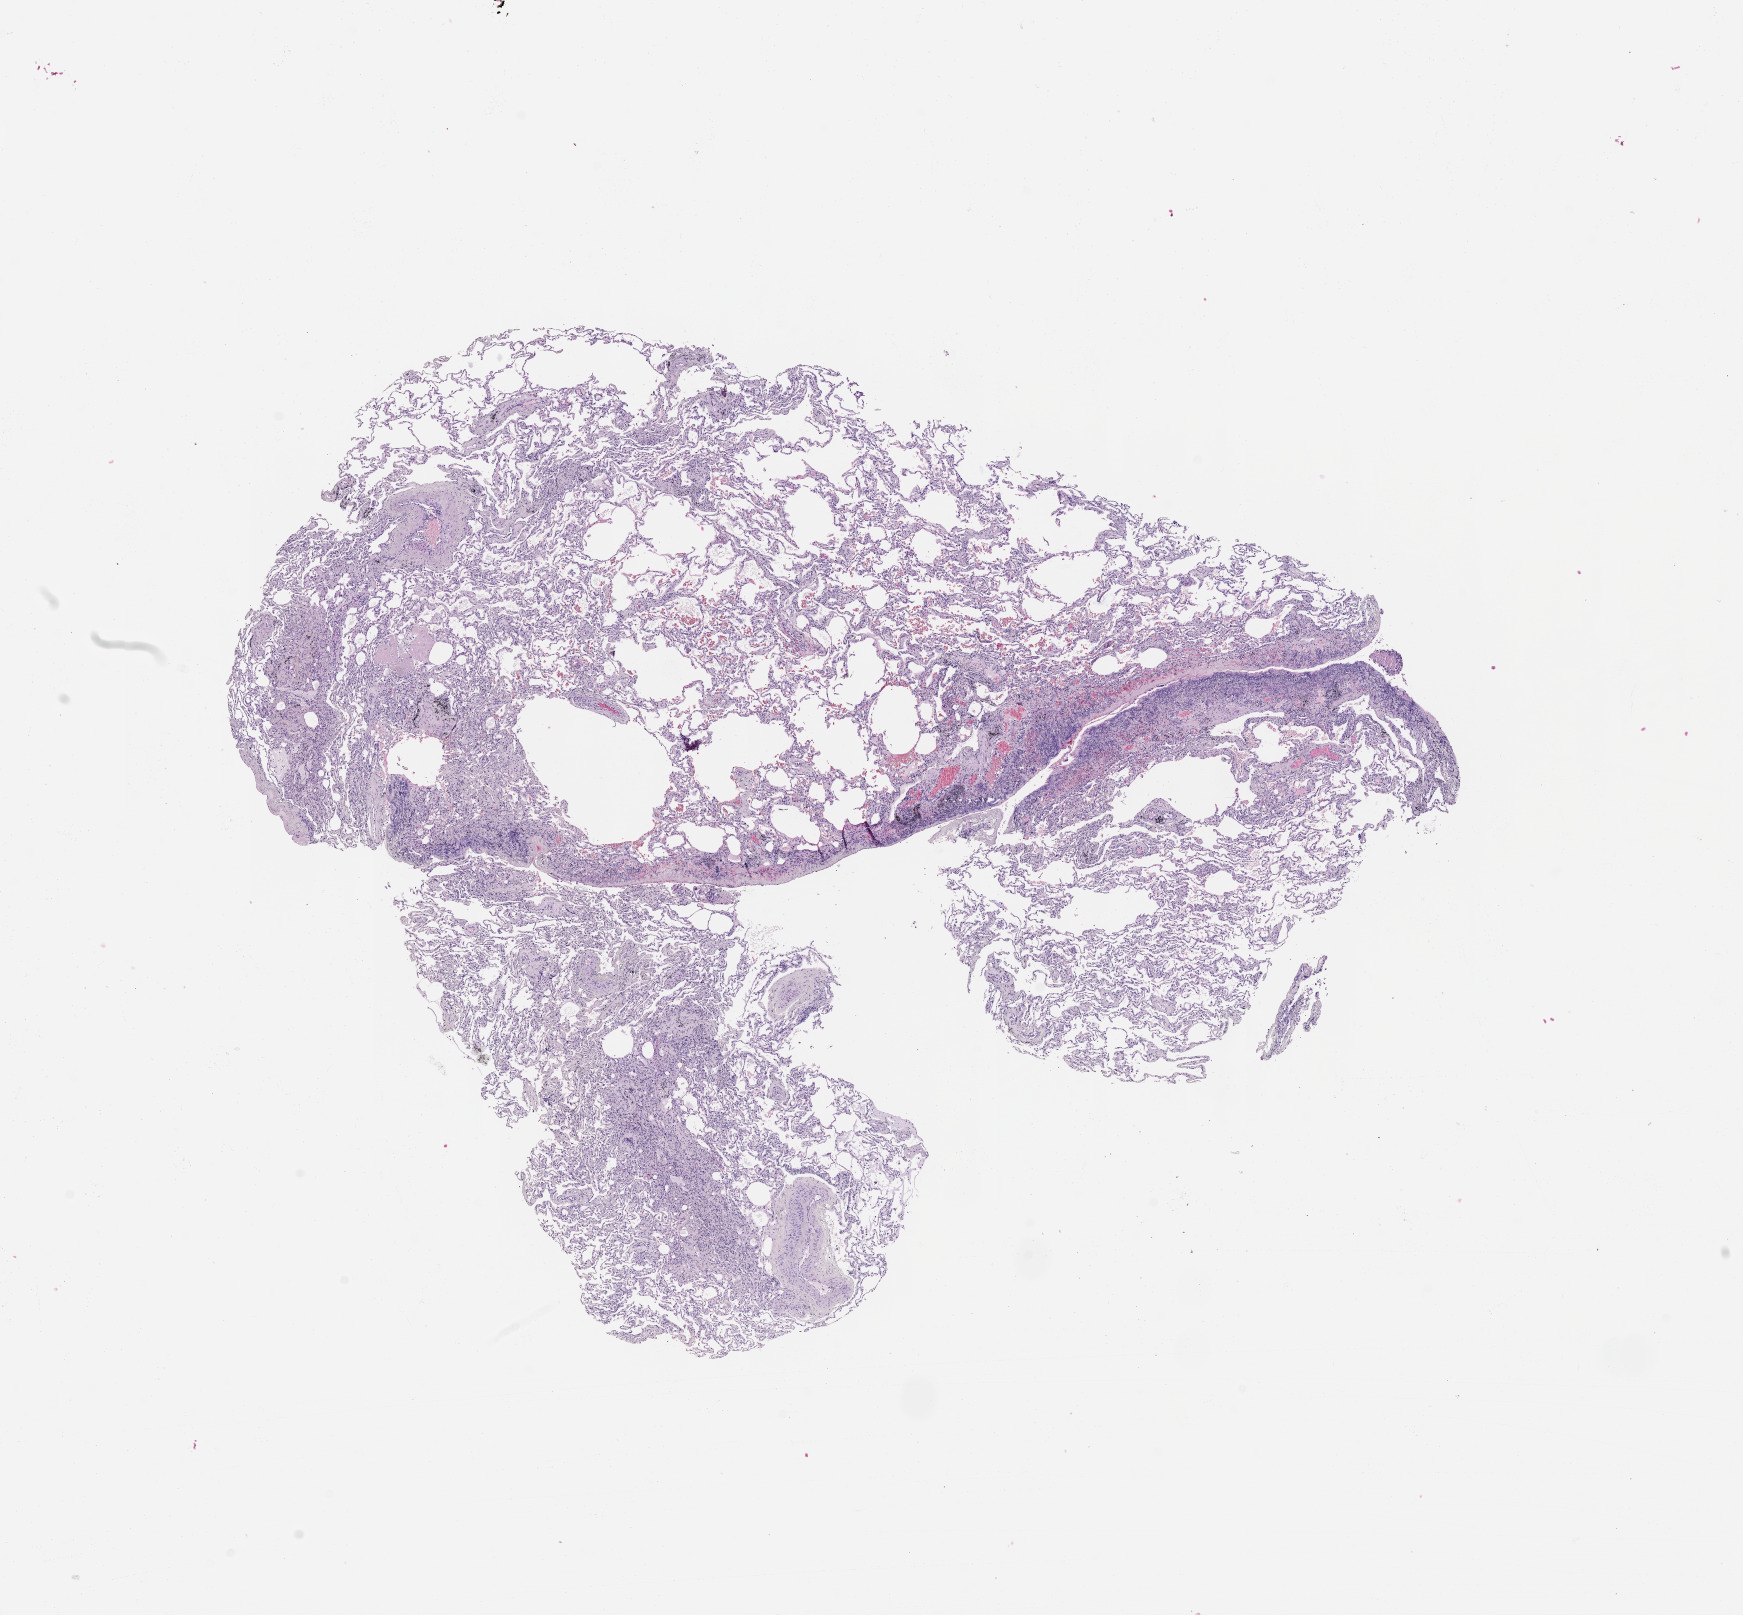
Whole-slide histology image, H&E-stained, whole scanned area (about 14.0 x 13.0 mm, acquisition: 20x scan) shown as a low-resolution overview. Normal (non-tumour) tissue sample, lung. Patient: male, age 60 years.
• this section: normal (non-tumour) tissue from the same patient
• patient diagnosis (cohort enrolment): squamous cell carcinoma (lung)